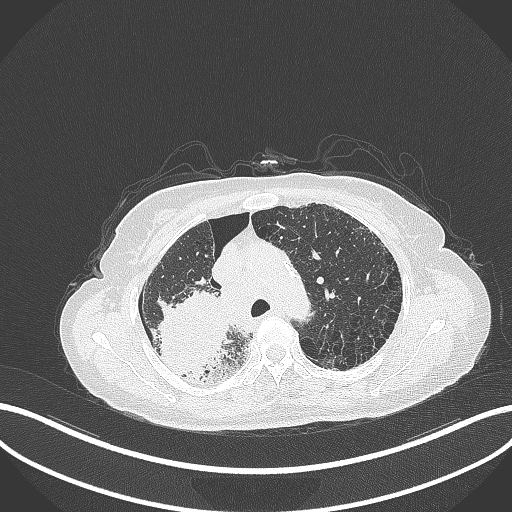
Chest CT, one axial slice. Position 254 of 408 along the scan axis. 120 kVp. Lung window (W 1500 / L -600 HU). 512 × 512 image matrix. Patient: female, 64 years. Case-level facts recorded for this patient, not image findings: clinical TNM (as recorded): T3 N3 M0.
Structures marked on this image (rectangle marked by the reading radiologist):
- lung tumour (recorded histology: squamous cell carcinoma): bounding box (x1, y1, x2, y2) in pixels: (148, 283, 235, 387)